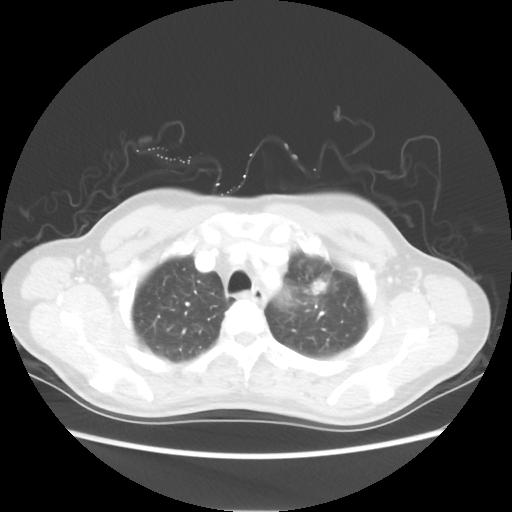
Chest CT, one axial slice. Position 44 of 54 along the scan axis. Reconstruction kernel STANDARD. Lung window (W 1500 / L -600 HU). 5 mm slice thickness. 512 × 512 image matrix, field of view 360 × 360 mm. Female patient, age 53 years. From the clinical record (not read from this slice): clinical TNM (as recorded): T1c N0 M0.
Structures marked on this image (bounding box drawn by a radiologist):
- lung tumour (recorded histology: adenocarcinoma): bounding box (x1, y1, x2, y2) in pixels: (304, 269, 327, 302)
- lung tumour (recorded histology: adenocarcinoma): (310, 280, 327, 295)